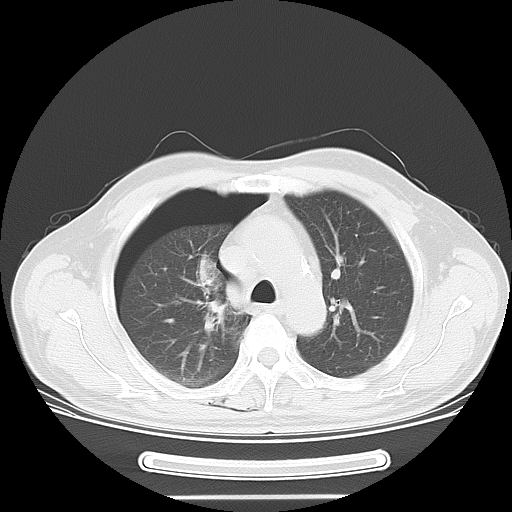
Chest CT, one axial slice; slice 41 of 57 in the series (ordered by position); reconstruction kernel LUNG; 120 kVp; lung window (W 1500 / L -600 HU); 5 mm slice thickness; 512 × 512 image matrix. Male patient, age 61 years. From the clinical record (not read from this slice): clinical TNM (as recorded): T1c N3 M1b.
Outlined on this slice (bounding box drawn by a radiologist):
- lung tumour (recorded histology: adenocarcinoma): bounding box (x1, y1, x2, y2) in pixels: (183, 252, 243, 341)